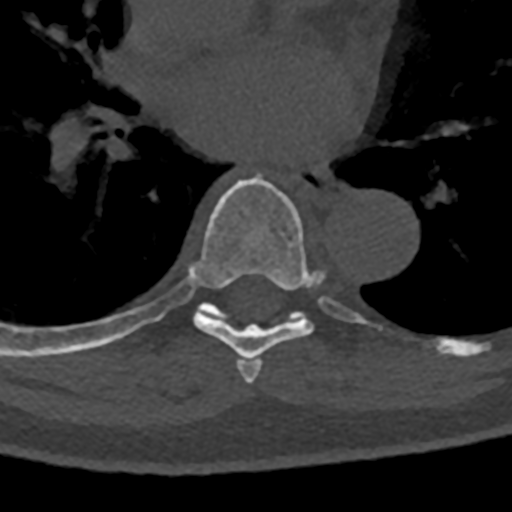
CT including the spine, one axial slice. Position 754 of 797 along the scan axis. Reconstruction kernel Br40s/3. 120 kVp. Bone window (W 1800 / L 400 HU). 512 × 512 image matrix. Male patient, age 74 years. From the clinical record (not read from this slice): primary cancer: renal; vertebrae with lytic lesions (as recorded): T10, L1, L2, L3, L4, L5.
Outlined on this slice (semi-automatically segmented with operator editing):
- T6 vertebra: box from (x=238, y=359) to (x=263, y=384) px
- T7 vertebra: (x=71, y=175)–(x=362, y=366)
- T8 vertebra: (x=70, y=304)–(x=430, y=353)